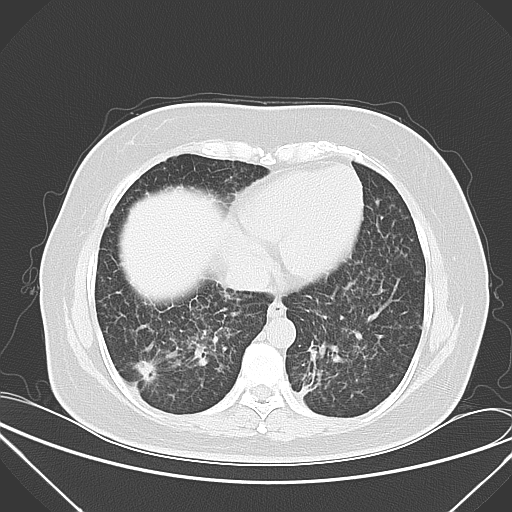
Chest CT, one axial slice. Position 16 of 52 along the scan axis. Lung window (W 1500 / L -600 HU). 5 mm slice thickness. 512 × 512 image matrix, field of view 386 × 386 mm. Patient: female, 50 years. From the clinical record (not read from this slice): clinical TNM (as recorded): T1c N0 M1a.
Outlined on this slice (rectangle marked by the reading radiologist):
- lung tumour (recorded histology: adenocarcinoma): box from (x=130, y=355) to (x=163, y=393) px